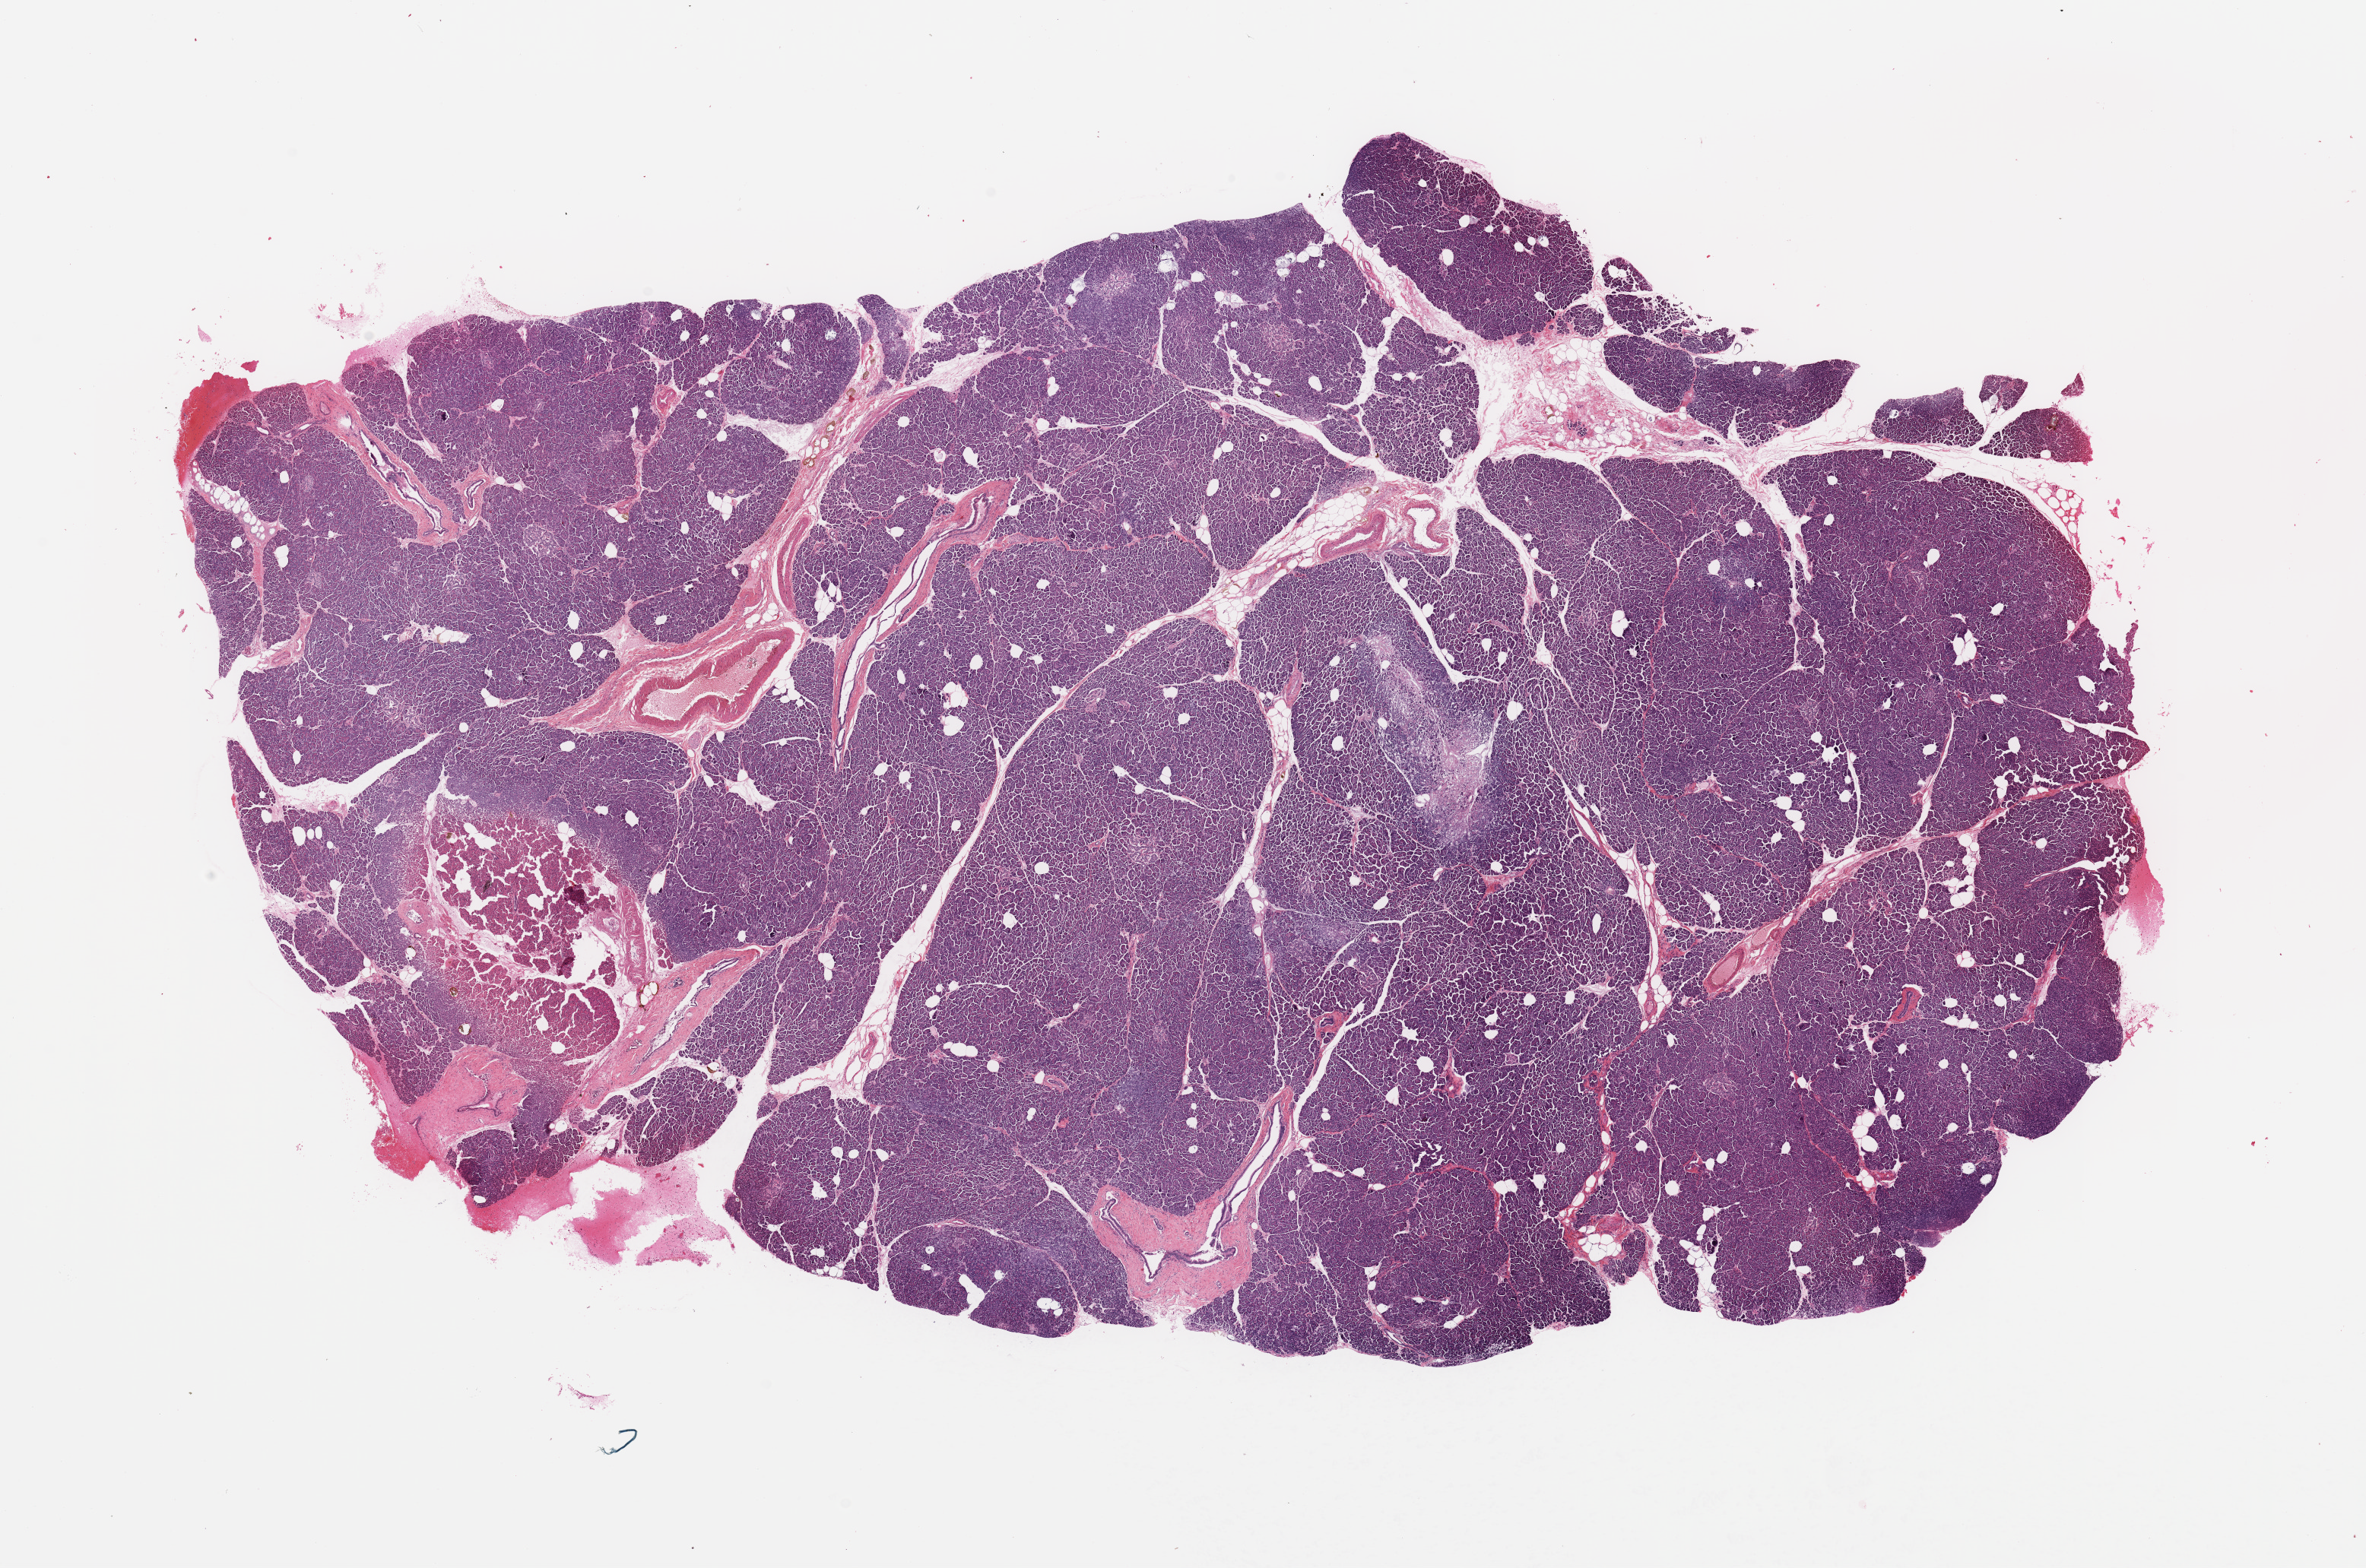
H&E-stained whole-slide image, a low-resolution overview of the entire scanned area, about 24.6 x 16.3 mm (from a 20x scan), normal (non-tumour) tissue sample, sampled site: pancreas. 64-year-old female patient.
• this section: normal (non-tumour) tissue from the same patient
• patient diagnosis: Infiltrating duct carcinoma, NOS